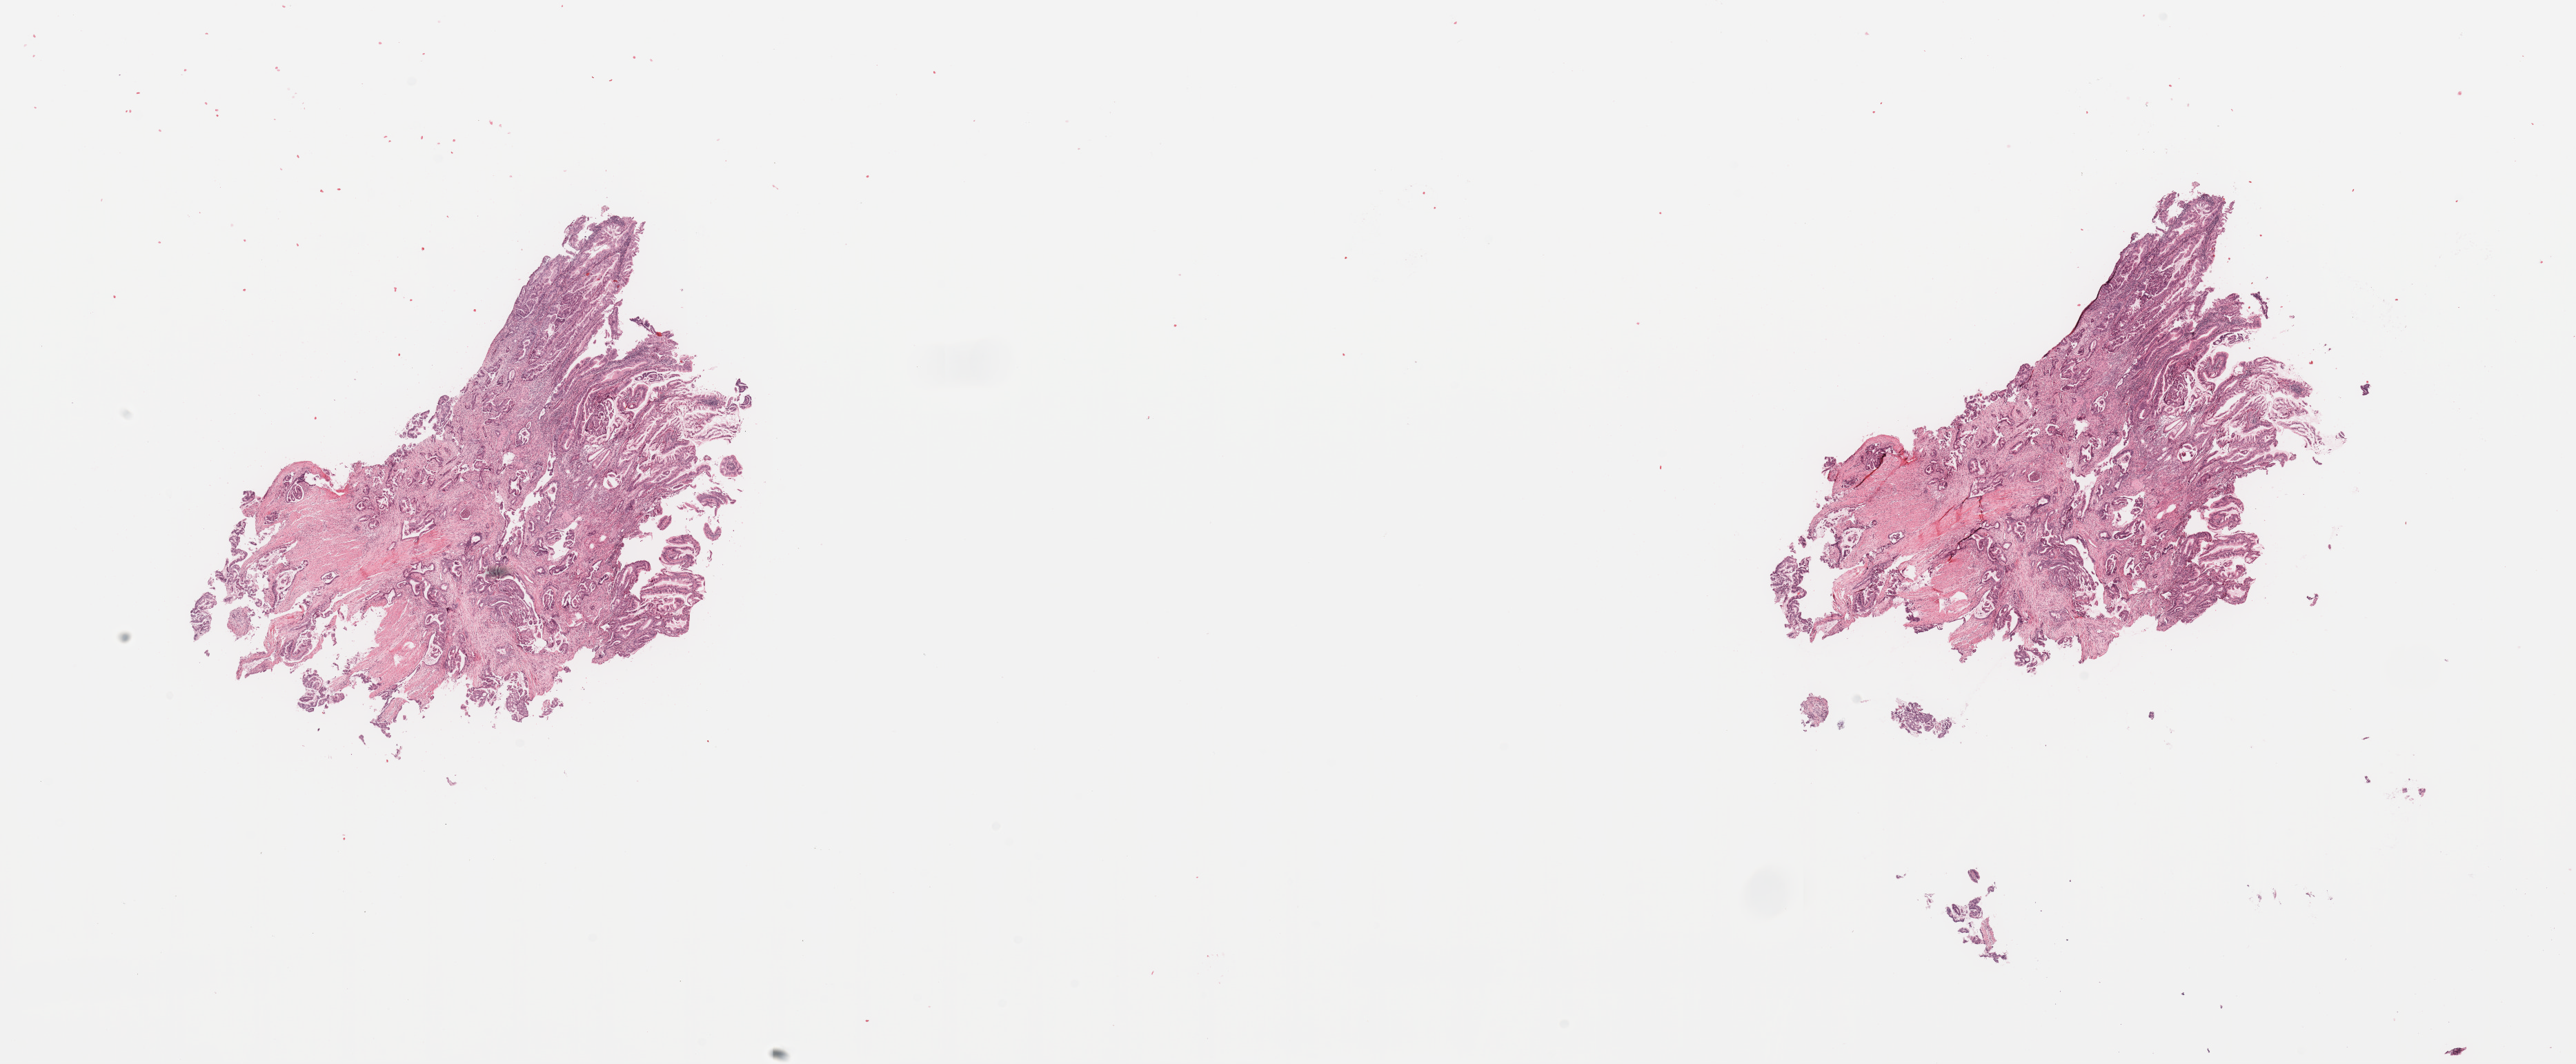
H&E whole-slide image, low-resolution overview of the scanned area, about 29.5 x 12.2 mm (slide scanned at 20x); tumour tissue sample, sampled site: pancreas. Female, 62 y/o. Histologic grade: G3 (poorly differentiated). Composition of this section per pathologist review: tumour nuclei 80%, necrosis 0%.
Primary tumour site (as recorded): head. Histologic diagnosis: Infiltrating duct carcinoma, NOS. AJCC pathologic stage: III.